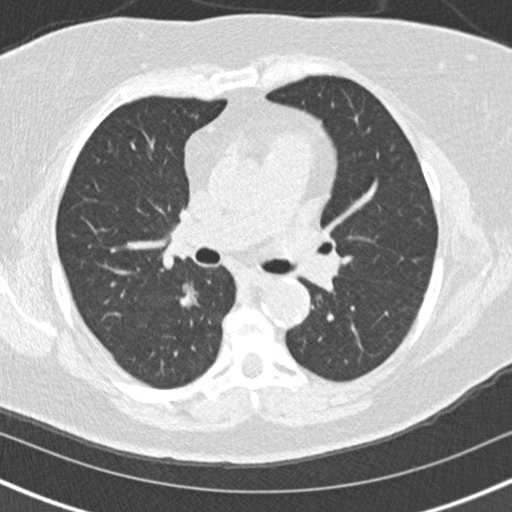
Low-dose screening chest CT, one axial slice. Reconstruction kernel B30f. 120 kVp. Lung window (W 1500 / L -600 HU). 512 × 512 image matrix, field of view 320 × 320 mm.
Annotated regions visible in this slice (expert manual segmentation):
- lesion 1 (tumor, lower lobe of right lung): bounding box [x1, y1, x2, y2] px = [180, 283, 199, 308]